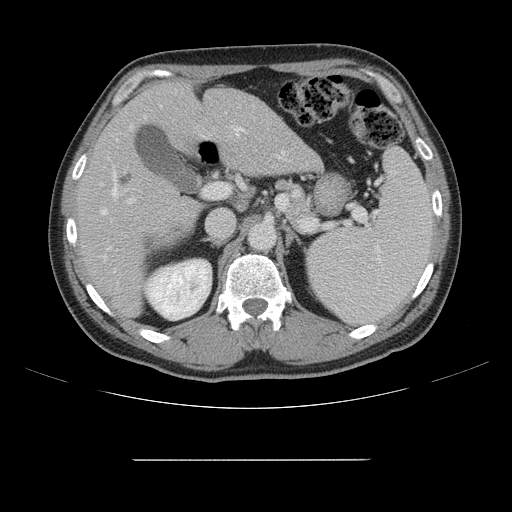
Contrast-enhanced abdominal CT, one axial slice; position 92 of 164 along the scan axis; intravenous contrast given; soft-tissue window (W 400 / L 40 HU); 2.5 mm slice thickness; 512 × 512 image matrix, field of view 404 × 404 mm. Male patient, age 54 years. Case-level facts recorded for this patient, not image findings: diagnosis: colorectal cancer liver metastases, imaged before liver resection; multiple liver metastases: yes; largest metastasis: 1 cm; disease in both lobes: no.
Structures marked on this image (manually delineated by an expert):
- hepatic veins: box from (x=101, y=133) to (x=285, y=260) px
- liver: (x=79, y=82)–(x=319, y=316)
- planned liver remnant (the part of the liver to remain after resection): (x=78, y=82)–(x=232, y=316)
- portal vein (with intrahepatic branches): (x=117, y=116)–(x=245, y=204)